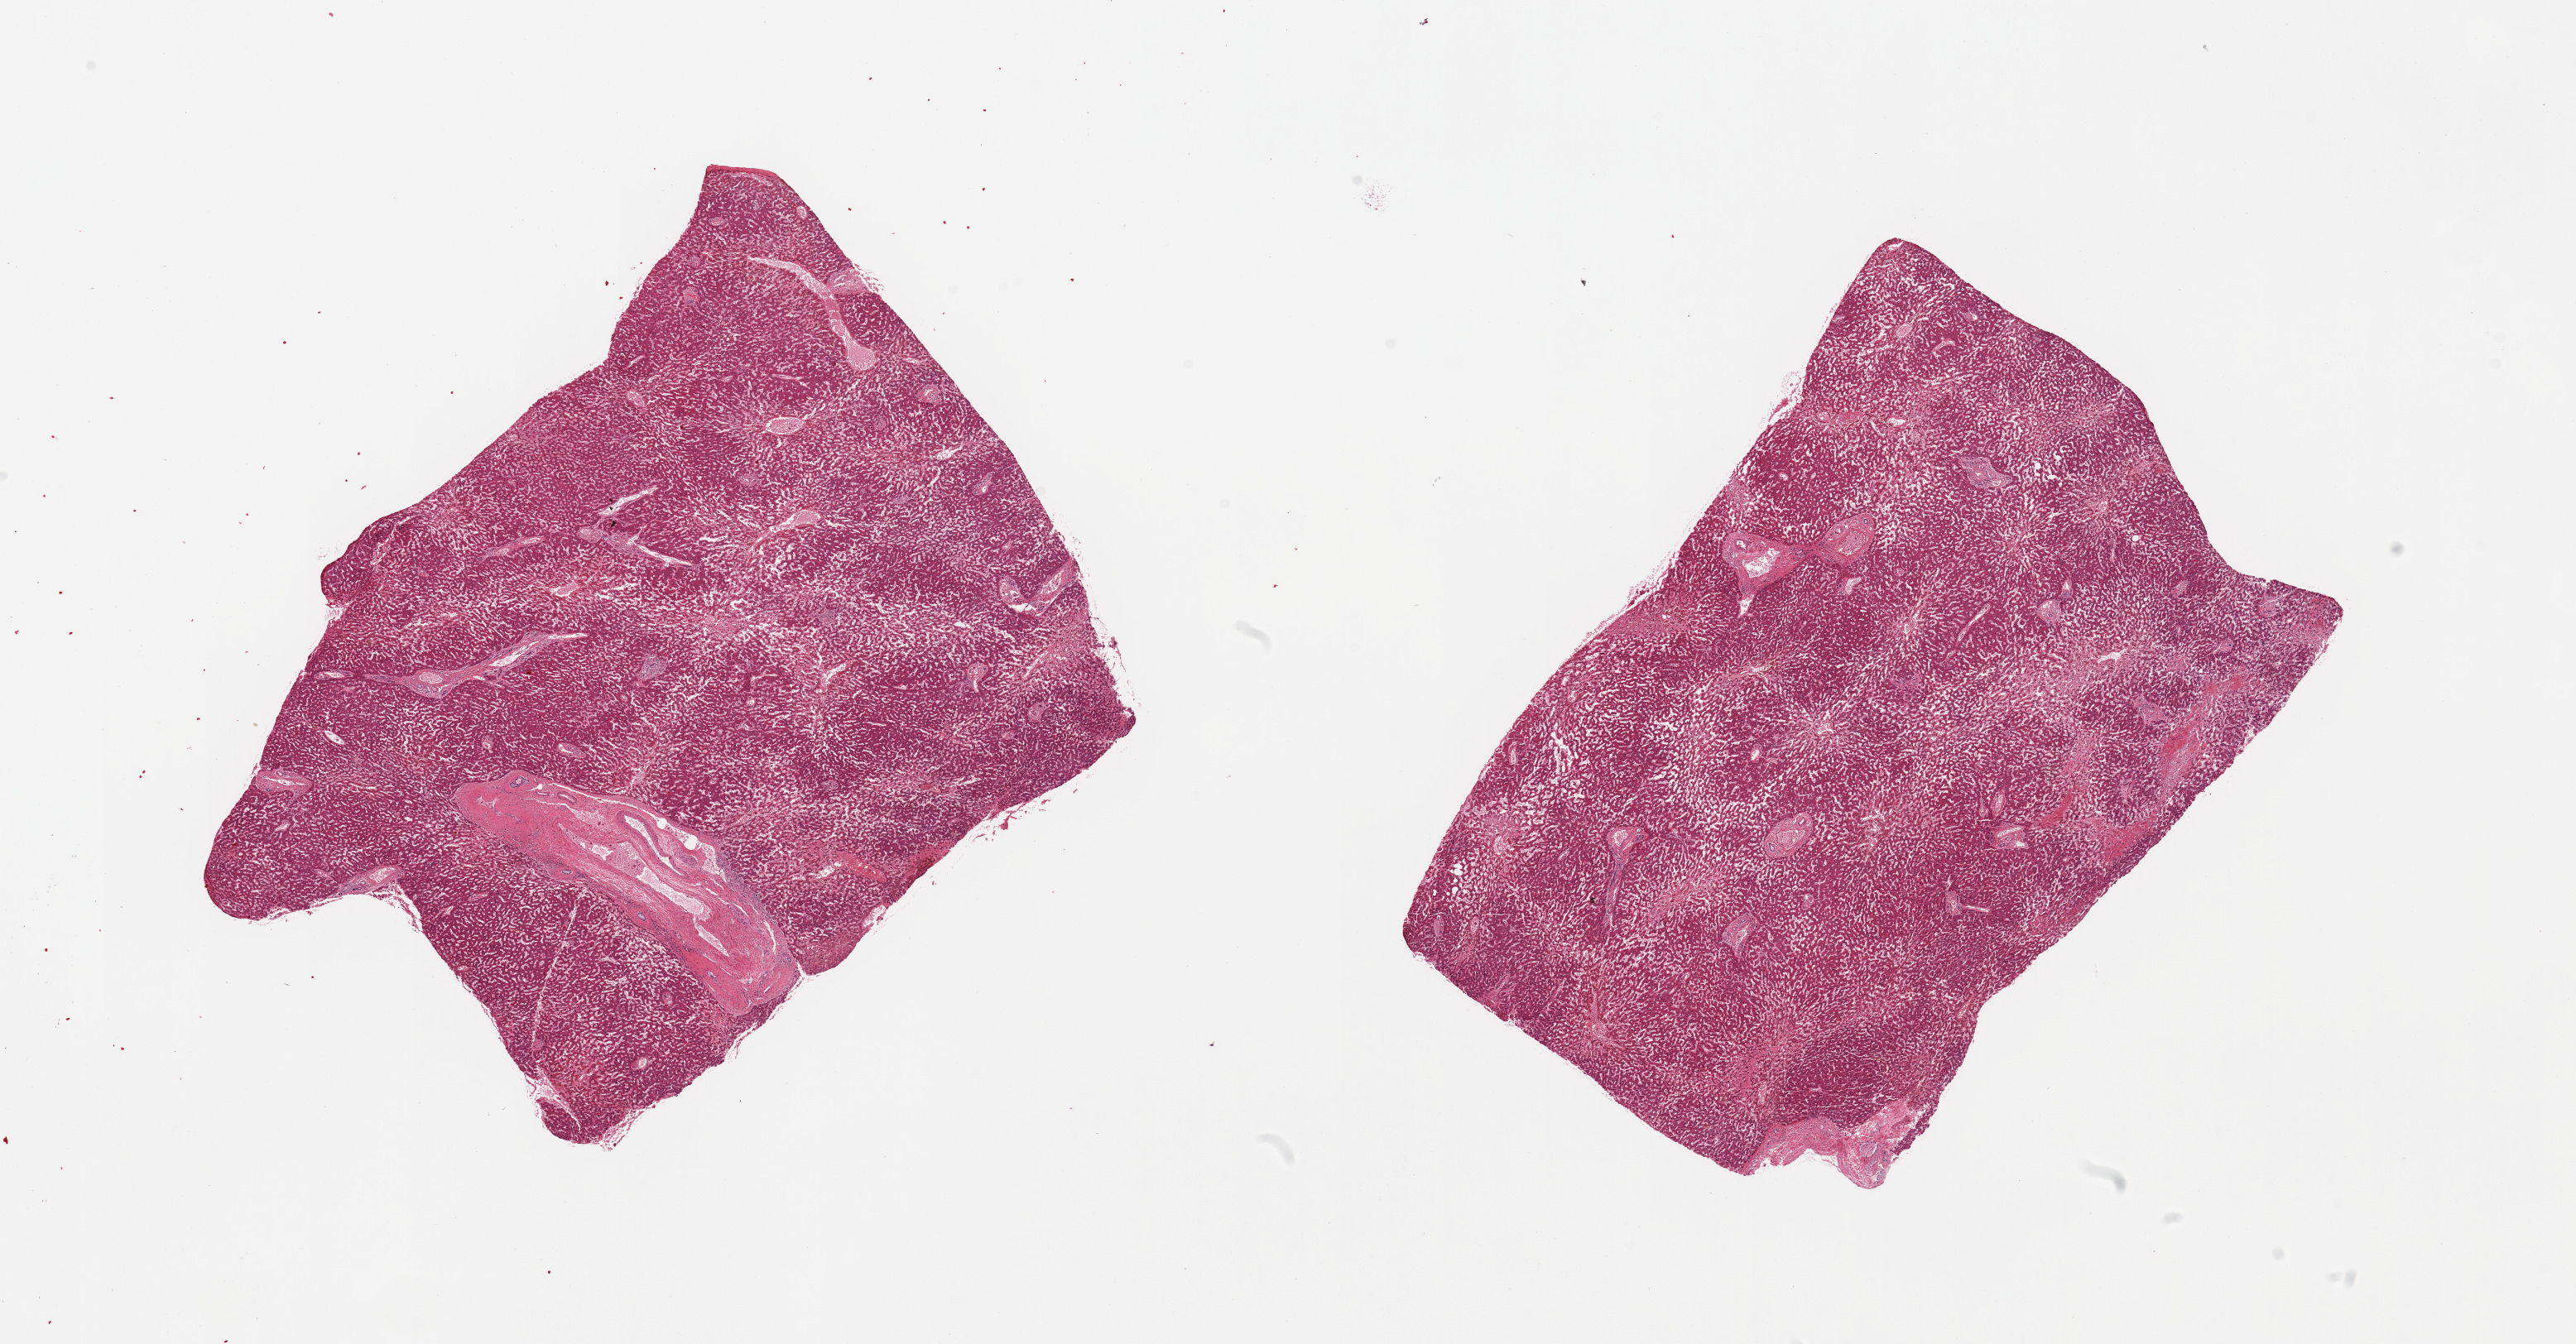
Digitized haematoxylin and eosin-stained section — shown as a low-resolution overview of the whole scanned area (about 24.6 x 12.8 mm). PAXgene-fixed paraffin-embedded (PFPE) section. Target tissue: liver. Donor tissue sample.
* review note (as recorded): 2 pieces, liver, moderate chronic passive congnestion, early fibrosis noted